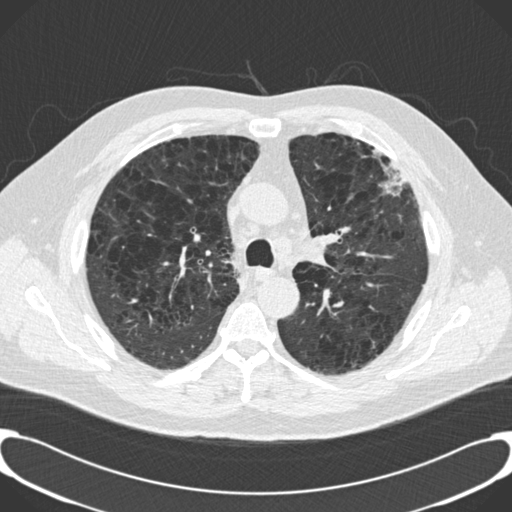
Low-dose screening chest CT, one axial slice; reconstruction kernel B30f; 120 kVp; lung window (W 1500 / L -600 HU); 2 mm slice thickness; 512 × 512 image matrix.
Annotated regions visible in this slice (expert manual segmentation):
- lesion 1 (tumor, upper lobe of left lung): bounding box [x1, y1, x2, y2] px = [379, 169, 408, 196]